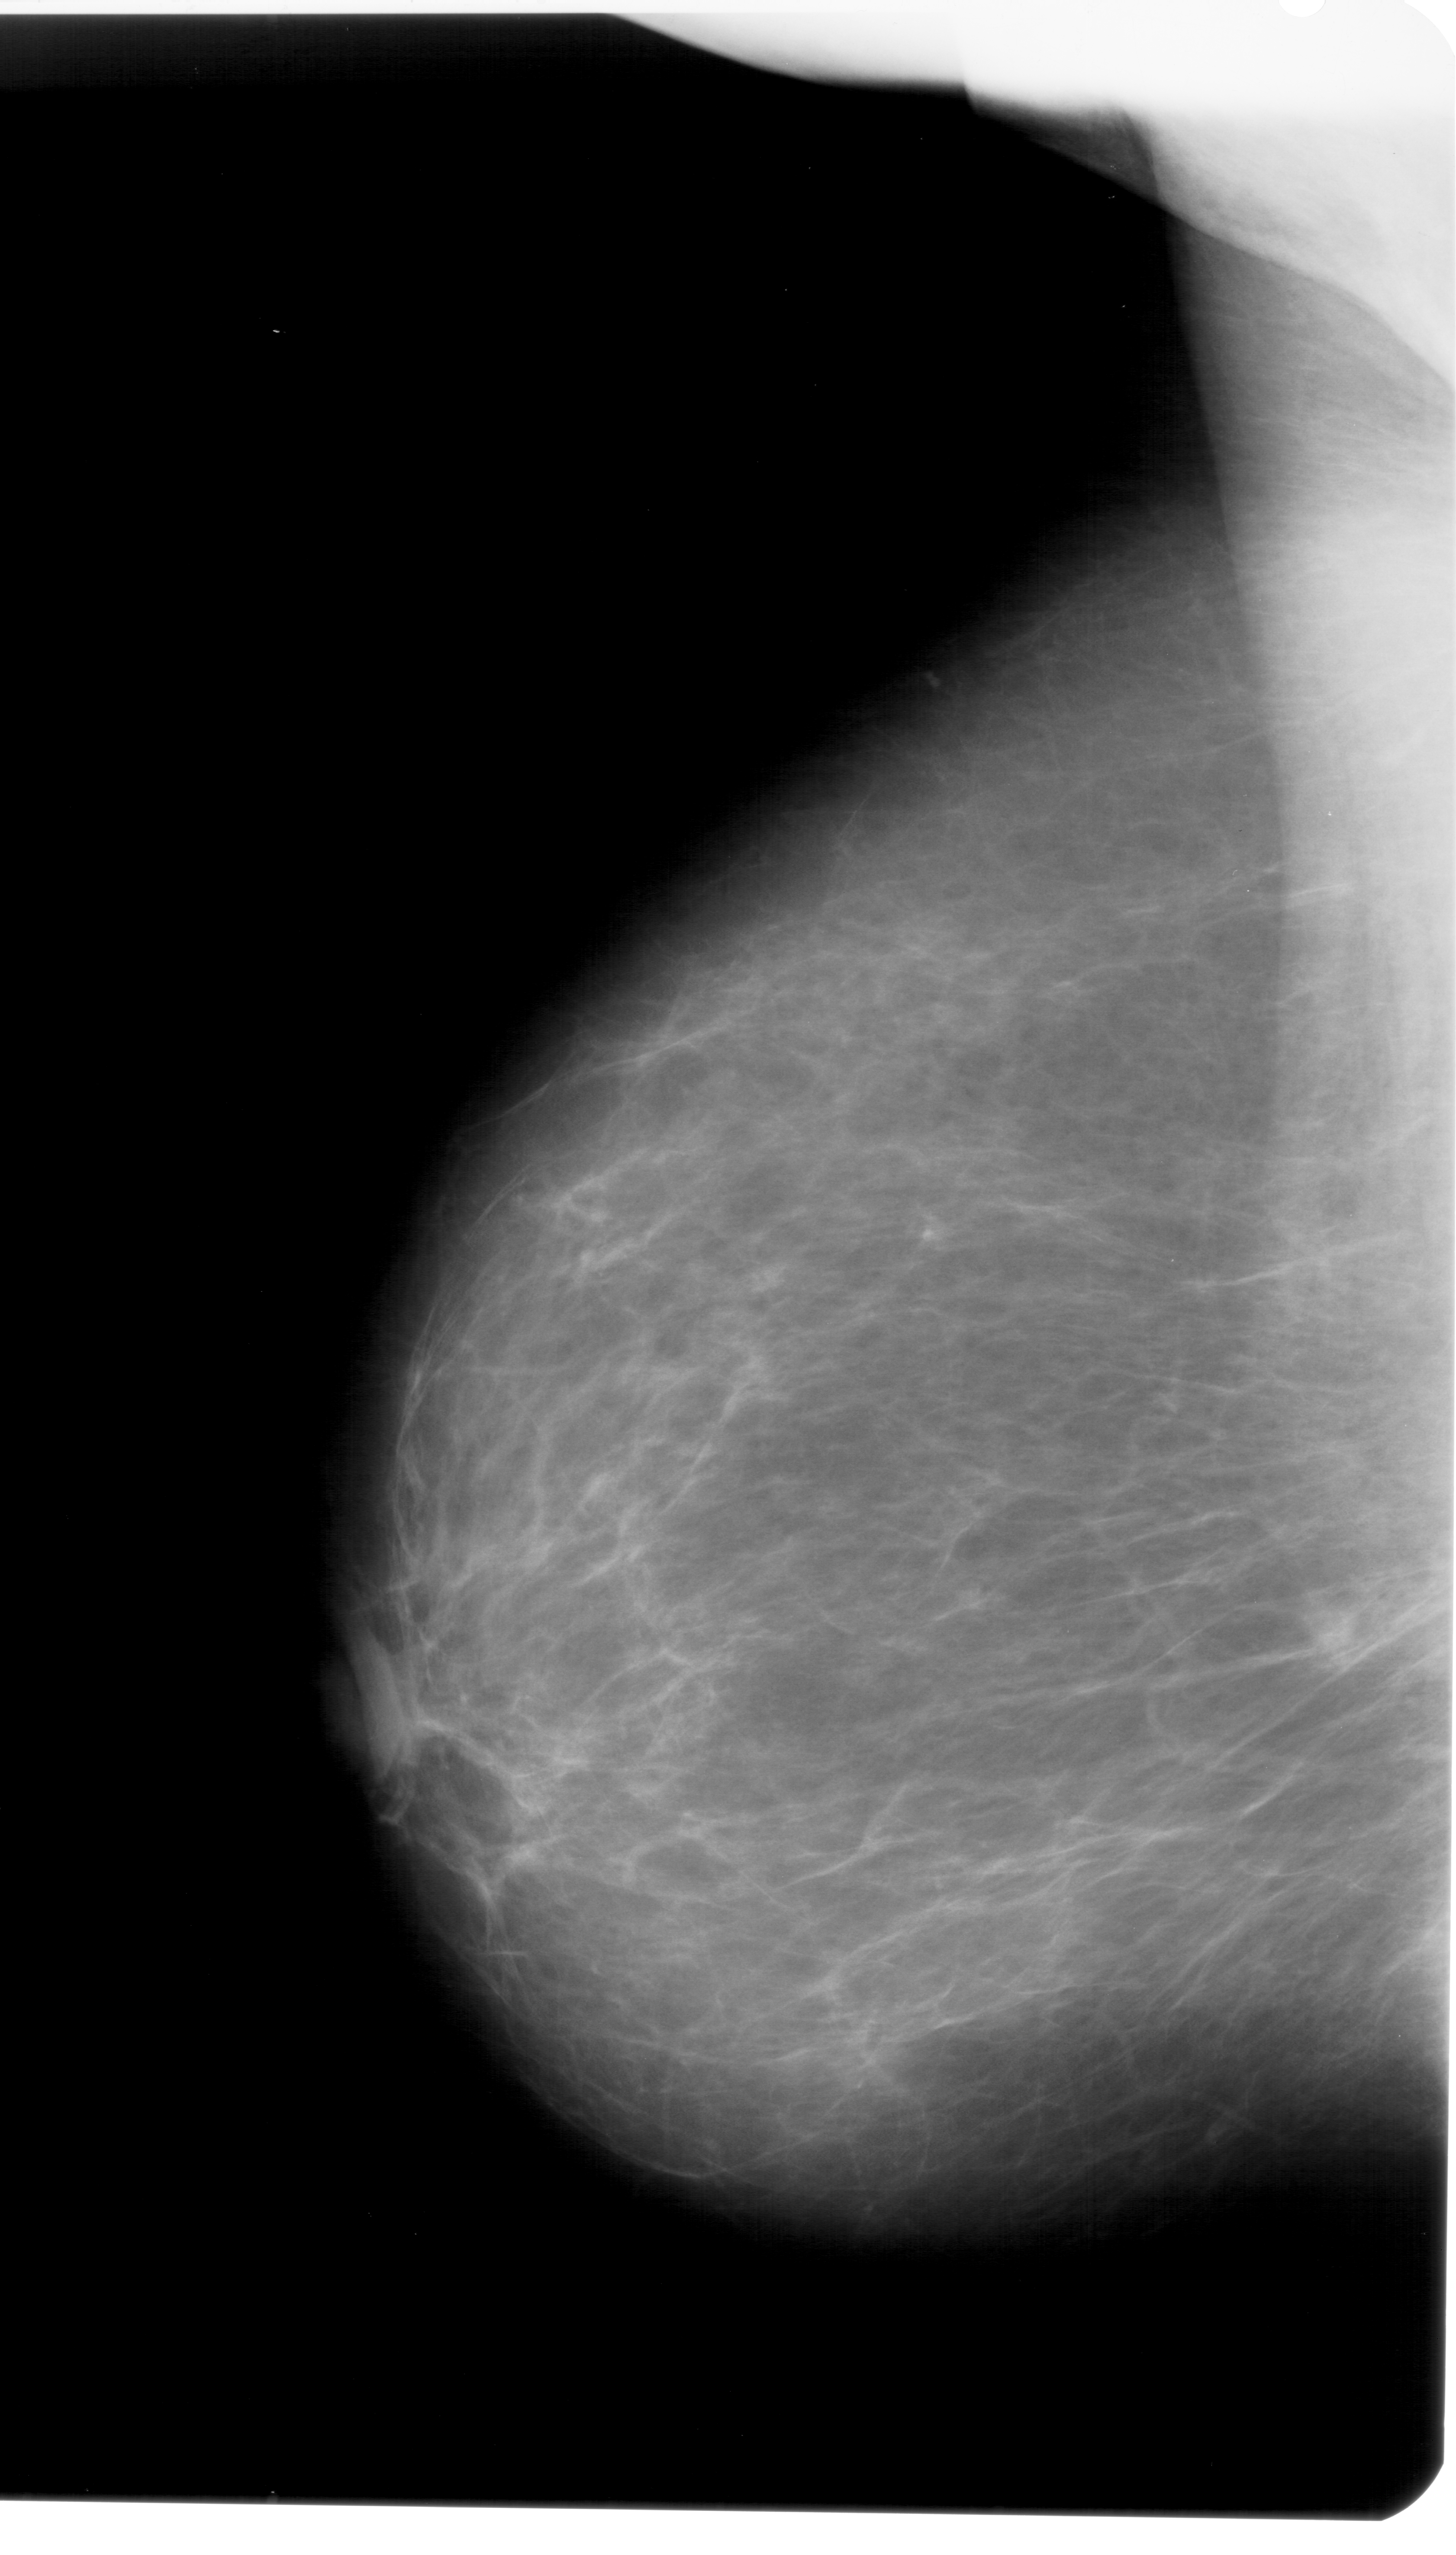
Mammogram (digitized film); left breast; mediolateral oblique (MLO) view; BI-RADS breast density category 2 (scale 1–4).
- Marked abnormality: mass, shape oval, margins ill defined; BI-RADS assessment category 5; subtlety rating 3 on a 1 (subtle) to 5 (obvious) scale; pathology (as recorded): malignant.